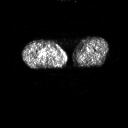
FDG PET of an extremity soft-tissue mass (from a PET/CT study), one axial slice; position 234 of 311 along the scan axis; 3.27 mm slice thickness; 128 × 128 image matrix, field of view 700 × 700 mm. Male patient, age 50 years. Case-level facts recorded for this patient, not image findings: histological type: undifferentiated - pleiomorphic; grade: high; site of the primary tumour: right thigh.
Outlined on this slice (expert contour drawn on MRI and transferred to this co-registered scan by the dataset authors):
- gross tumour volume including surrounding oedema: bounding box <42,52,48,57> (left, top, right, bottom; pixels)